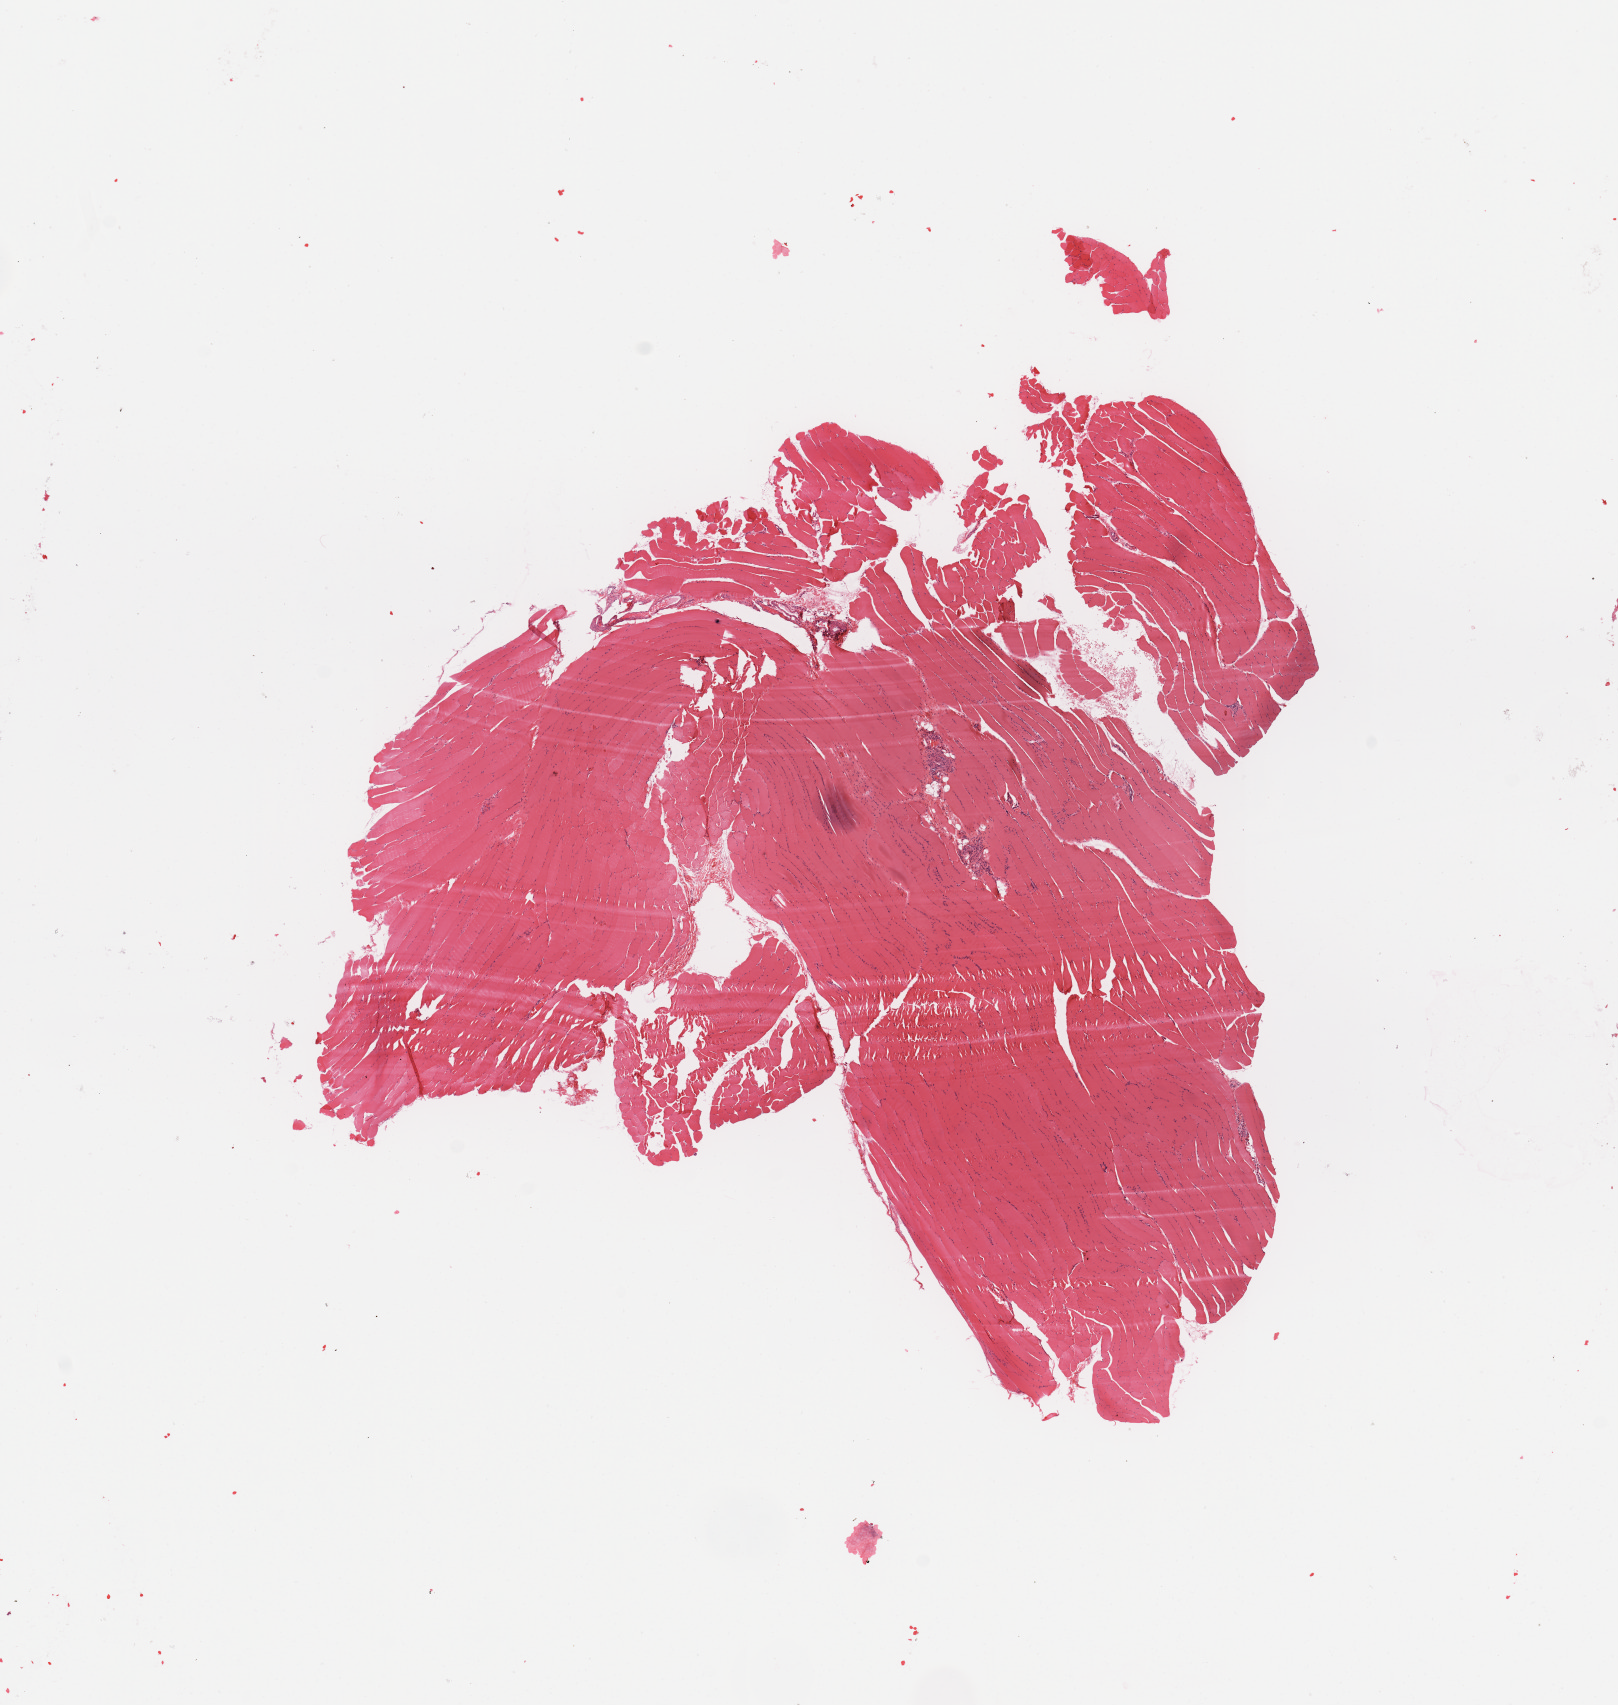
Whole-slide histology image, H&E — low-resolution overview of the scanned area, about 12.8 x 13.5 mm (acquisition: 20x scan); normal (non-tumour) tissue sample. 42-year-old male patient.
- this section: normal (non-tumour) tissue from the same patient
- patient diagnosis (cohort enrolment): sarcoma (site not recorded at cohort level)